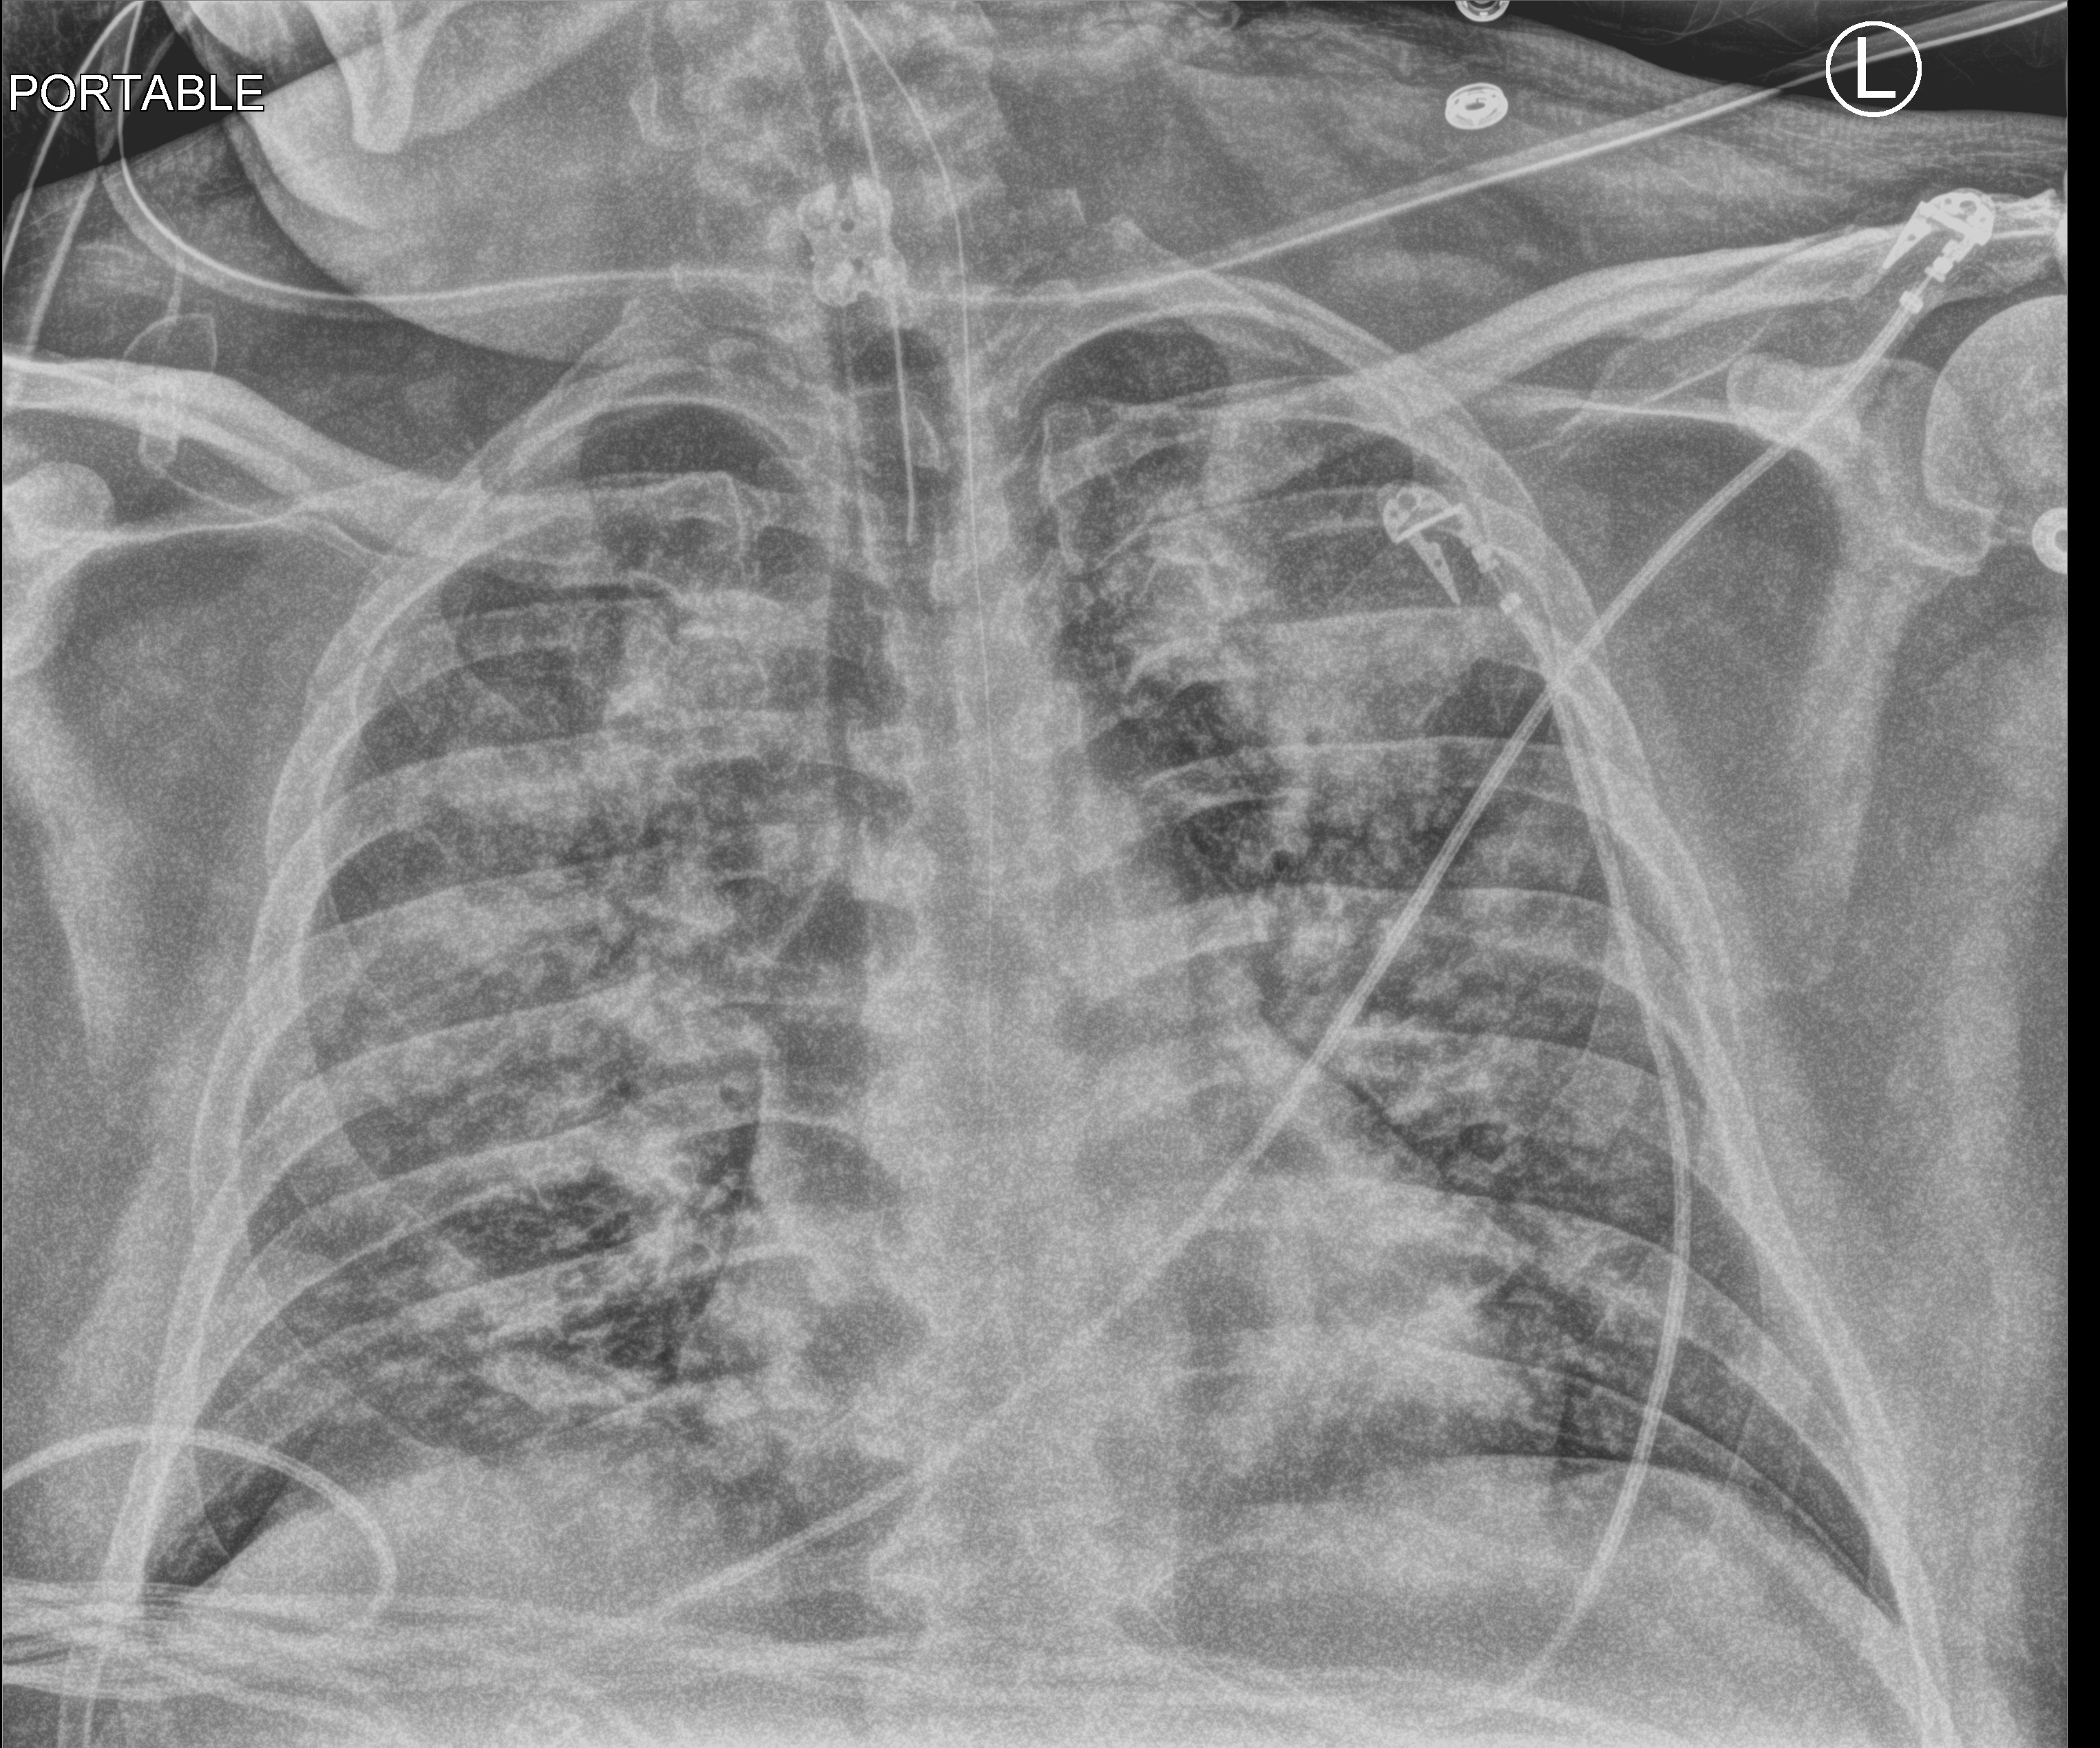
Chest X-ray (portable), anteroposterior (AP) projection. Patient hospitalised with COVID-19; male, aged 18–59 years.
Admission-level facts for this patient (not findings on this image; timing relative to this image not recorded): admitted to intensive care during this hospital stay: yes.